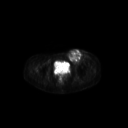
FDG PET of an extremity soft-tissue mass (from a PET/CT study), one axial slice. Position 70 of 267 along the scan axis. 3.27 mm slice thickness. 128 × 128 image matrix, field of view 600 × 600 mm. Female patient, age 24 years. From the clinical record (not read from this slice): histological type: leiomyosarcoma; grade: high; site of the primary tumour: groin.
Outlined on this slice (expert contour drawn on MRI and transferred to this co-registered scan by the dataset authors):
- gross tumour volume including surrounding oedema: bounding box <66,49,91,65> (left, top, right, bottom; pixels)
- gross tumour volume (mass): <66,49,83,64>